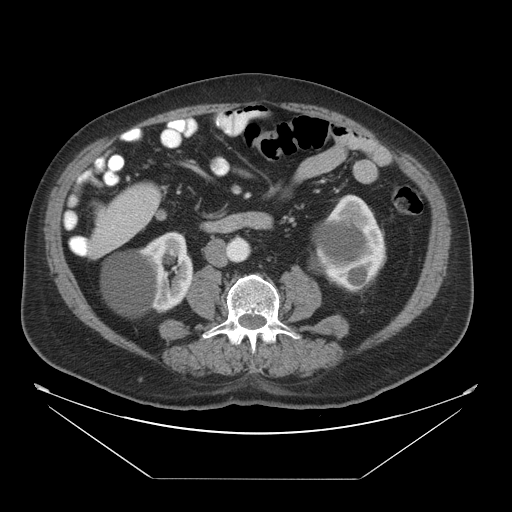
Contrast-enhanced abdominal CT, one axial slice. Slice 10 of 45 in the series (ordered by position). Intravenous contrast given. Soft-tissue window (W 400 / L 40 HU). 5 mm slice thickness. 512 × 512 image matrix, field of view 463 × 463 mm. Male patient, age 87 years. Case-level facts recorded for this patient, not image findings: diagnosis: colorectal cancer liver metastases, imaged before liver resection; multiple liver metastases: no; largest metastasis: 4.5 cm; disease in both lobes: yes.
Outlined on this slice (expert manual segmentation):
- liver: bounding box [x1, y1, x2, y2] px = [89, 183, 161, 258]